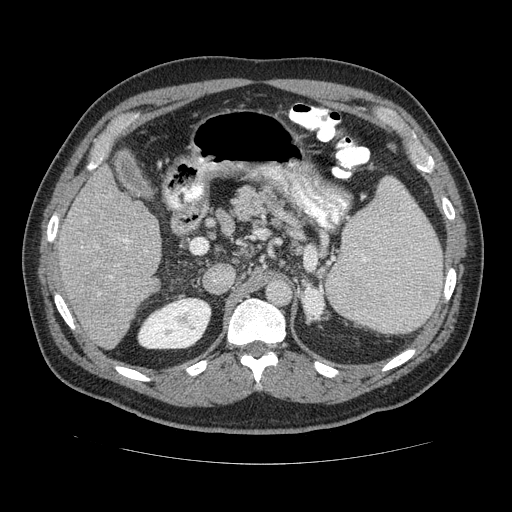
Contrast-enhanced abdominal CT (liver protocol), one axial slice; slice 74 of 113 in the series (ordered by position); reconstruction kernel STANDARD; soft-tissue window (W 400 / L 40 HU); 512 × 512 image matrix, field of view 400 × 400 mm. From the clinical record (not read from this slice): diagnosis: hepatocellular carcinoma (patient treated with transarterial chemoembolisation; whether this scan precedes or follows treatment is not stated here); TNM stage (as recorded): Stage-II; Child-Pugh class: B; tumour differentiation: moderately differentiated; tumour nodularity: multinodular.
Outlined on this slice (semi-automatically segmented with operator editing):
- liver parenchyma outside the tumour (the mass and vessels are separate outlines, so this box may not span the whole liver): bounding box <50,166,162,348> (left, top, right, bottom; pixels)
- liver vessels: <81,239,145,296>